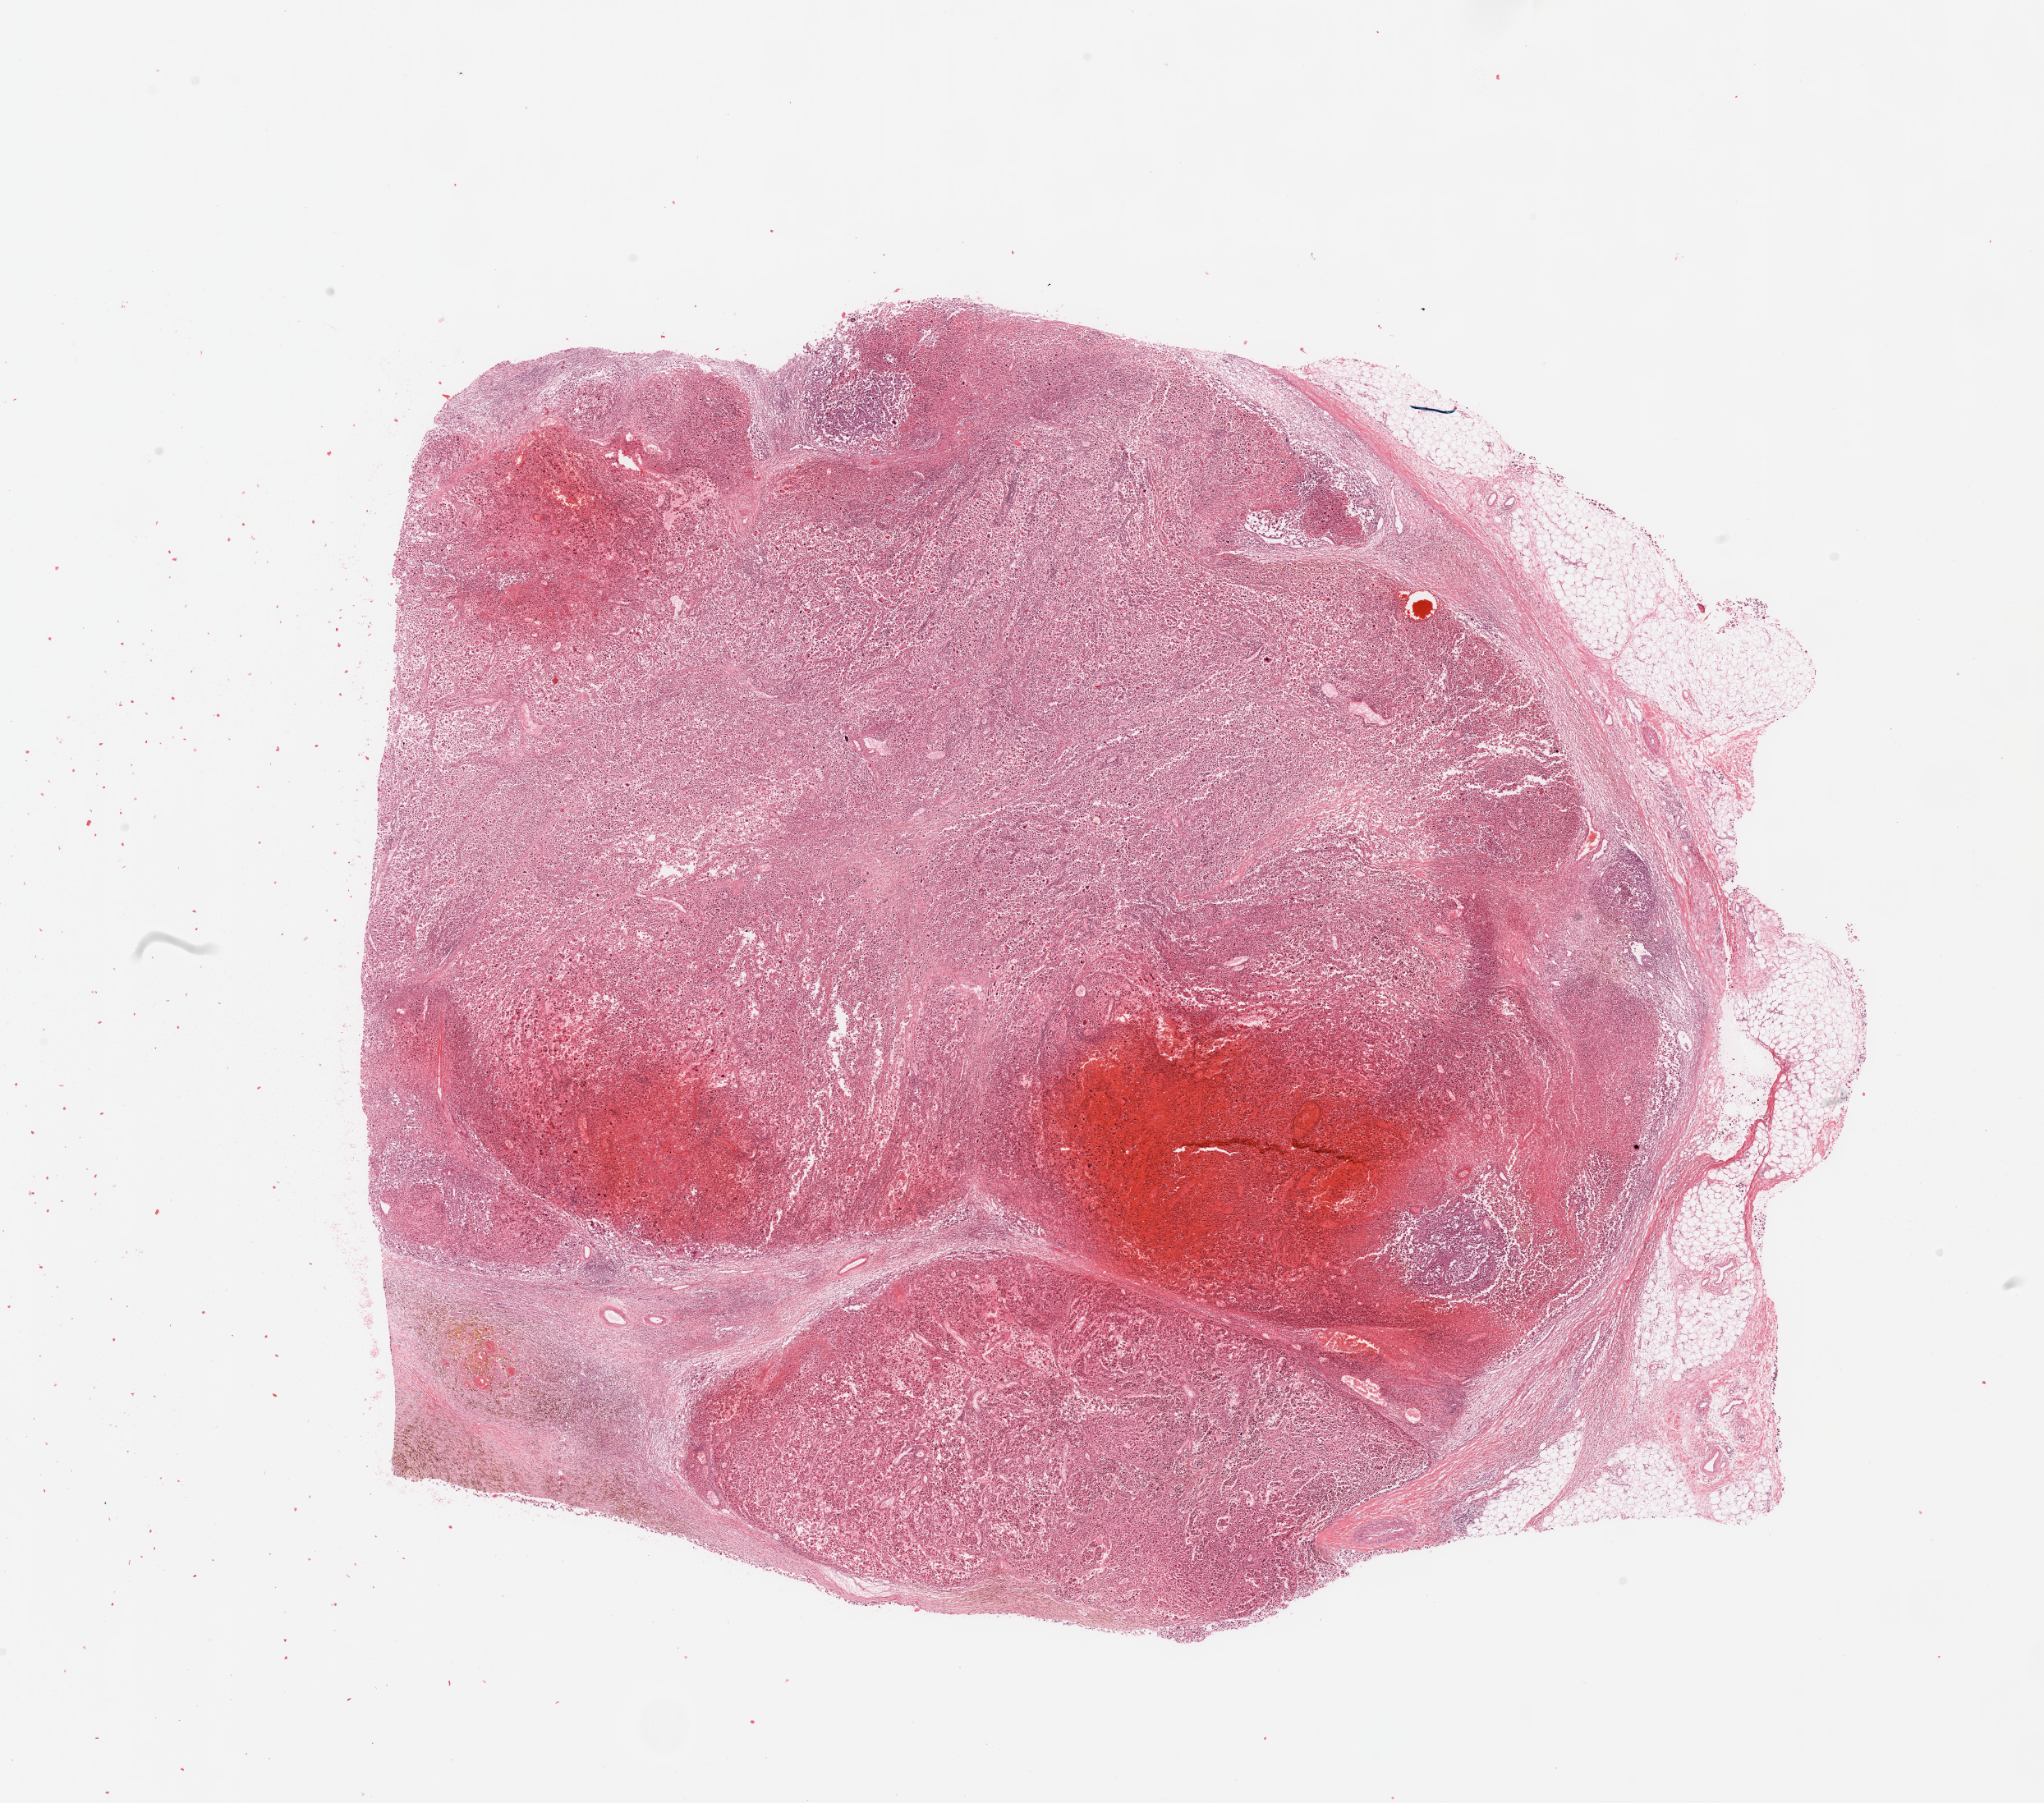
Digitized H&E tissue section (whole slide), shown as a low-resolution overview of the whole scanned area (about 19.7 x 17.4 mm, from a 20x scan), melanoma tumour tissue; sampled site not recorded. Male, 69 y/o.
Histologic diagnosis: Malignant melanoma, NOS. AJCC pathologic stage: IIIC.